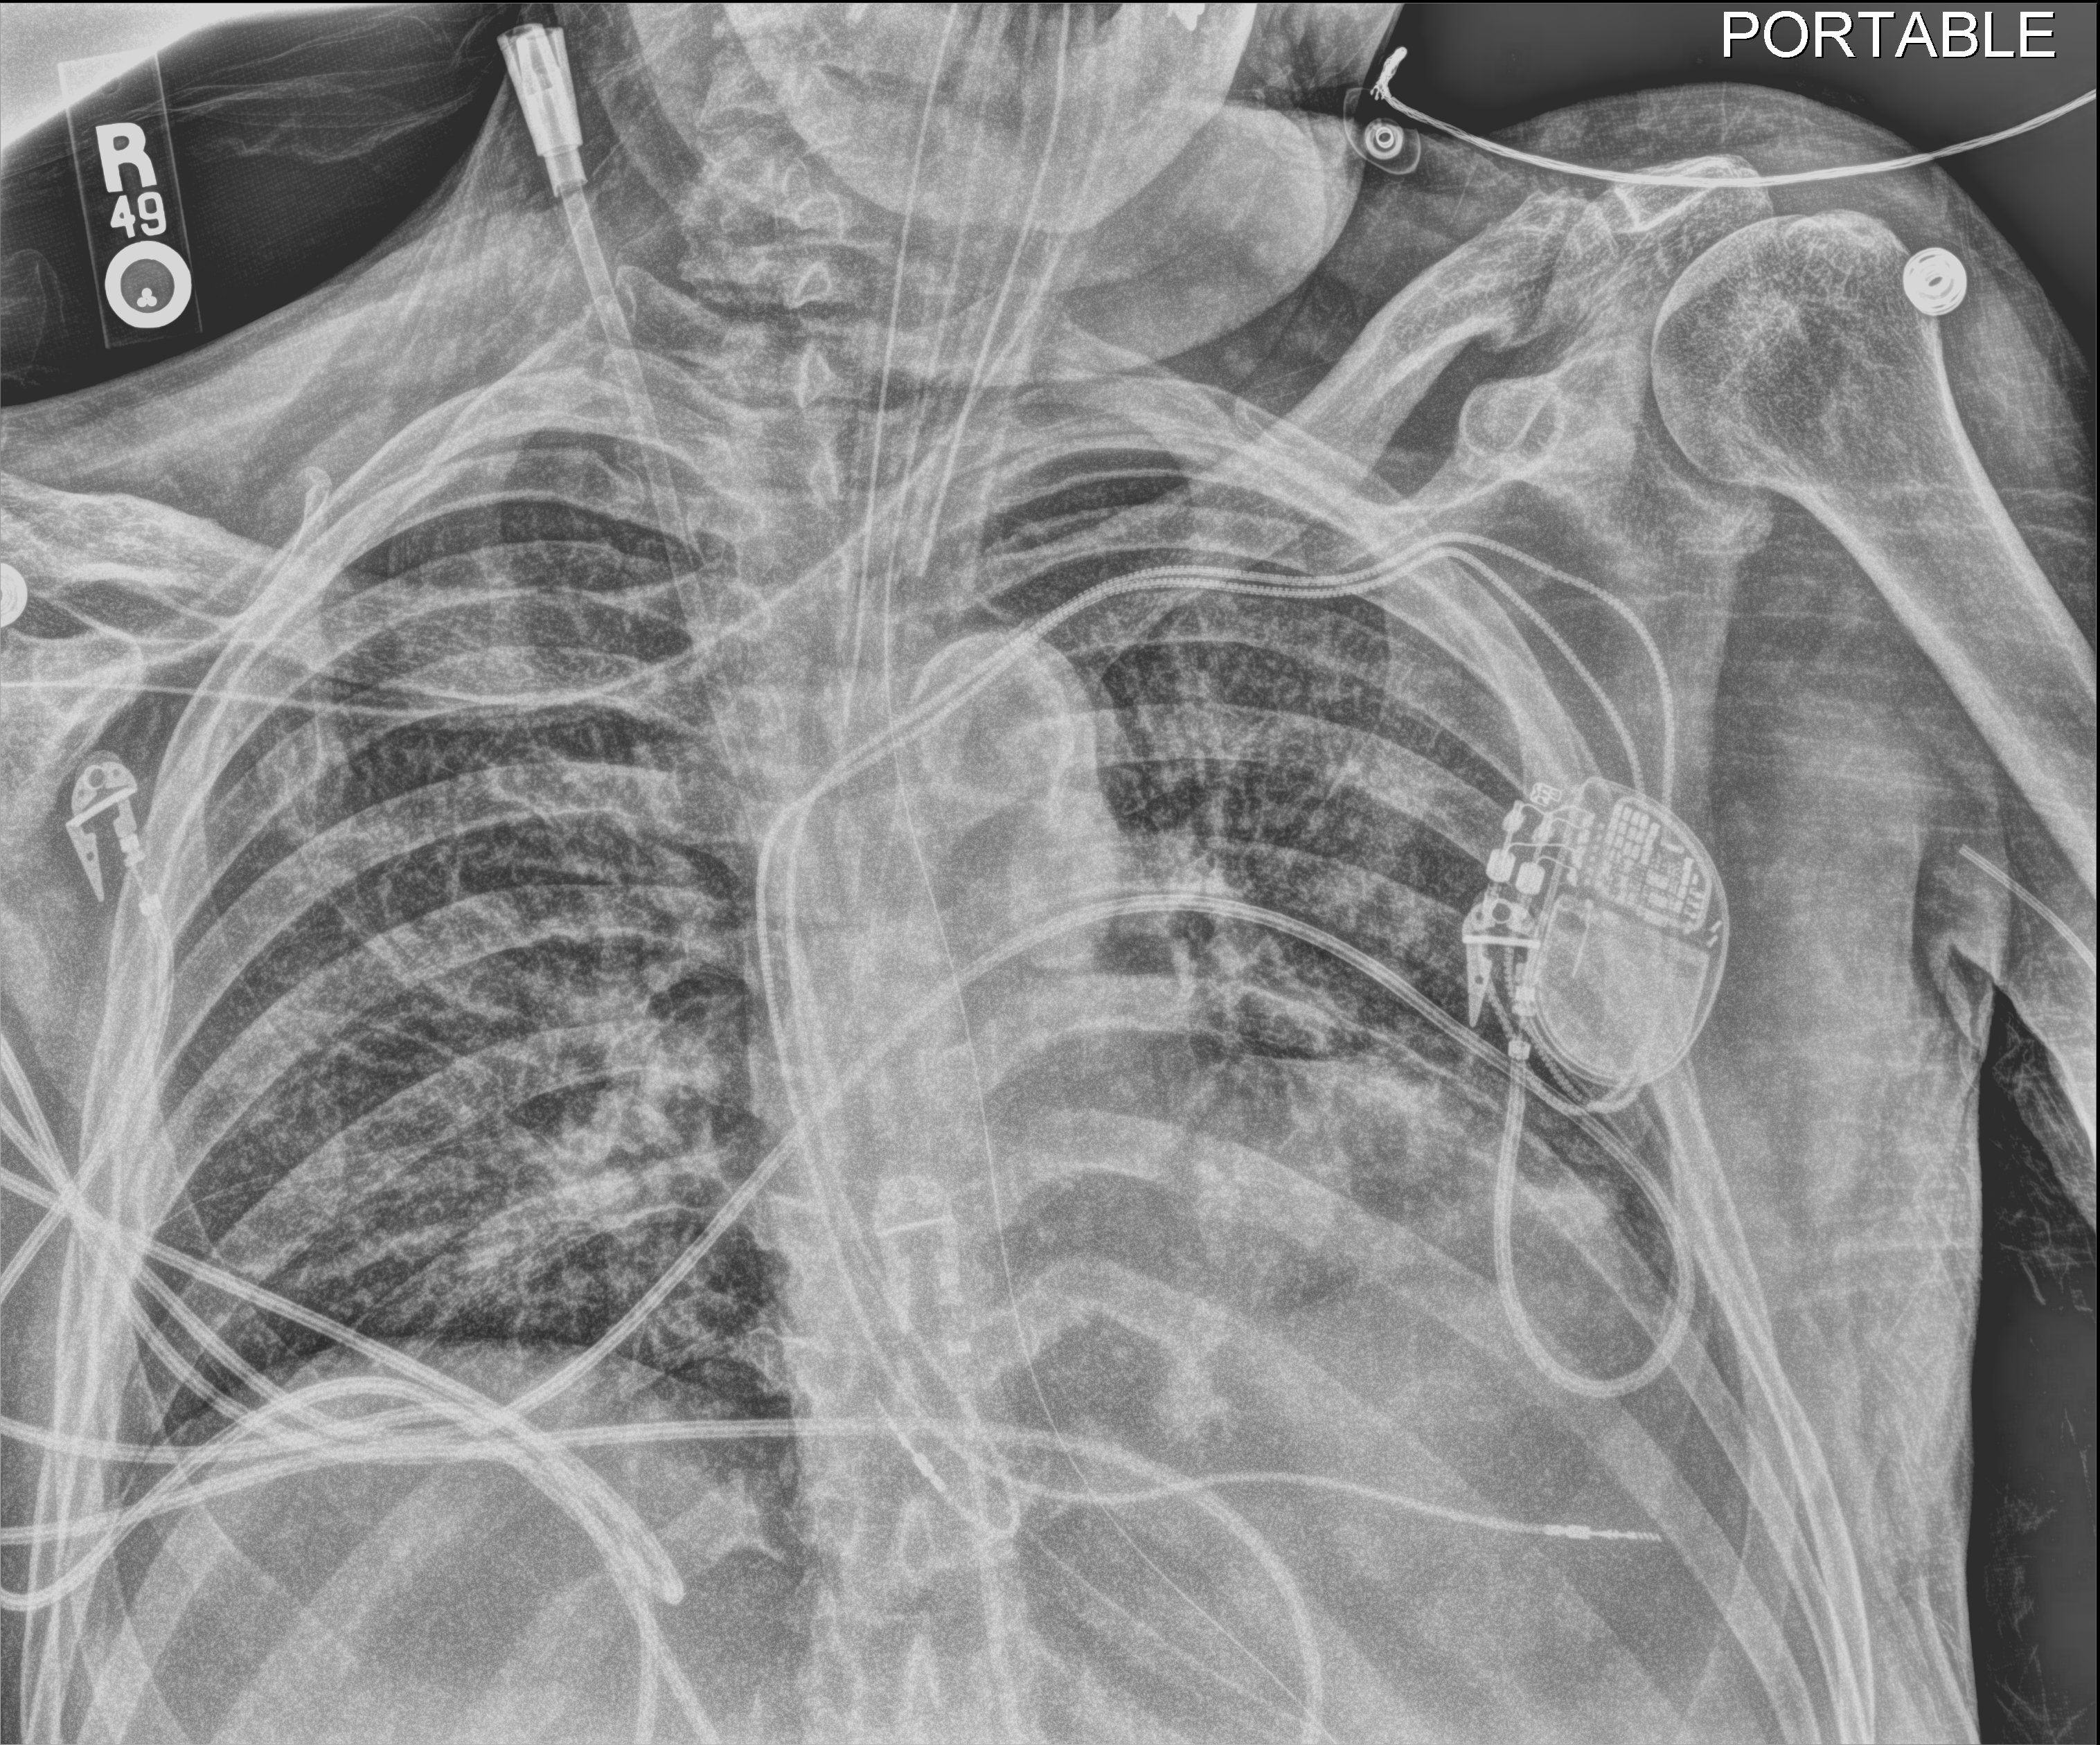
Portable chest radiograph. Patient hospitalised with COVID-19; male, aged 60–74 years.
Admission-level facts for this patient (not findings on this image; timing relative to this image not recorded):
- length of hospital stay: 41 days
- admitted to intensive care during this hospital stay: yes
- mechanically ventilated during this hospital stay: yes